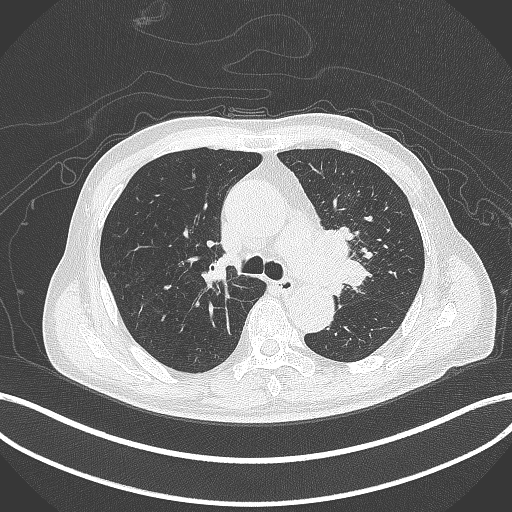
Chest CT, one axial slice; position 285 of 417 along the scan axis; reconstruction kernel B70f; 120 kVp; lung window (W 1500 / L -600 HU); 1 mm slice thickness; 512 × 512 image matrix, field of view 400 × 400 mm. Patient: male, 77 years. From the clinical record (not read from this slice): clinical TNM (as recorded): T3 N1 M0.
Structures marked on this image (rectangle marked by the reading radiologist):
- lung tumour (recorded histology: adenocarcinoma): bounding box <311,222,368,297> (left, top, right, bottom; pixels)